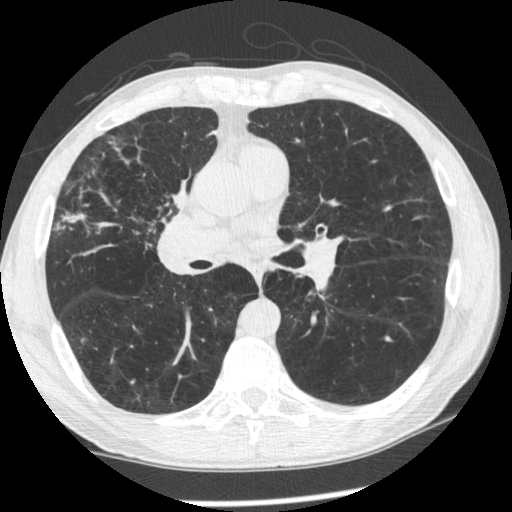
Low-dose screening chest CT, one axial slice; position 126 of 261 along the scan axis; 120 kVp; lung window (W 1500 / L -600 HU); 1.25 mm slice thickness; 512 × 512 image matrix, field of view 340 × 340 mm.
Annotated regions visible in this slice (outlined manually by an expert reader):
- lesion 1 (tumor, upper lobe of right lung): bounding box [x1, y1, x2, y2] px = [173, 180, 189, 208]